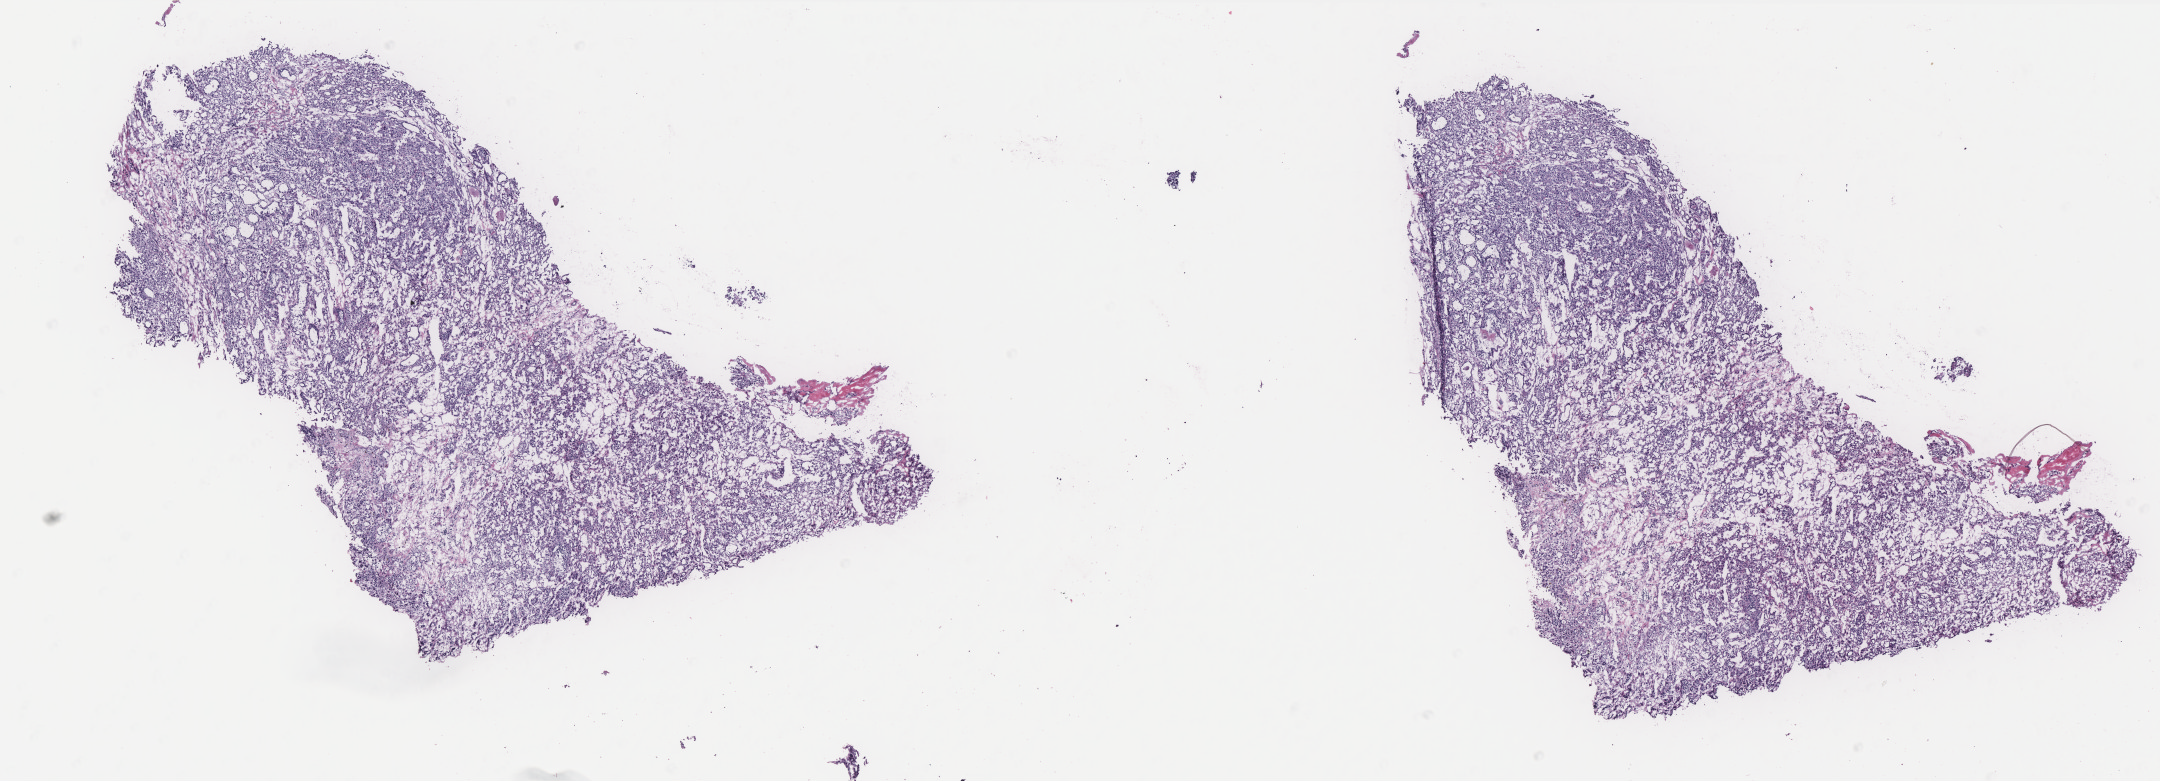
Whole-slide histology image, H&E-stained, a low-resolution overview of the entire scanned area, about 17.3 x 6.3 mm (slide scanned at 40x); frozen section from the bottom of the tissue portion; sample: primary tumour, thyroid. Female, age 54 years at initial diagnosis. Pathologist review of this section (percent, as recorded): tumour cells 70%, tumour nuclei 70%, normal cells 20%, stromal cells 10%, necrosis 0%. Inflammatory infiltration, as recorded: lymphocyte infiltration 4%, monocyte infiltration 0%, neutrophil infiltration 0%.
- TNM: T2 N0 M0
- diagnosis: Follicular carcinoma, minimally invasive (thyroid gland)
- AJCC pathologic stage: II (7th edition)